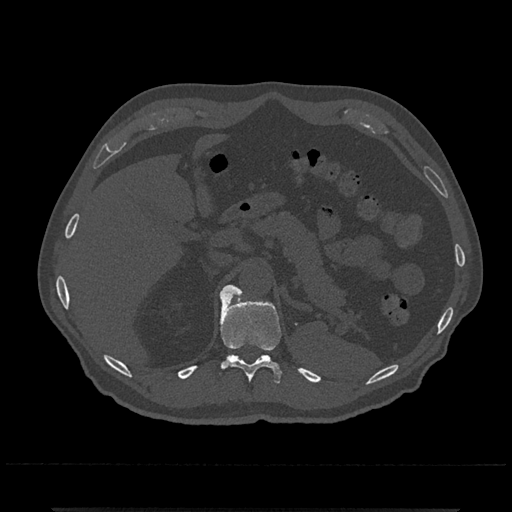
CT including the spine, one axial slice; 120 kVp; bone window (W 1800 / L 400 HU); 0.5 mm slice thickness; 512 × 512 image matrix, field of view 393 × 393 mm. Patient: male, 67 years. From the clinical record (not read from this slice): primary cancer: prostate.
Structures marked on this image (semi-automatically segmented with operator editing):
- T11 vertebra: box from (x=219, y=292) to (x=282, y=400) px
- T12 vertebra: (x=221, y=285)–(x=243, y=297)